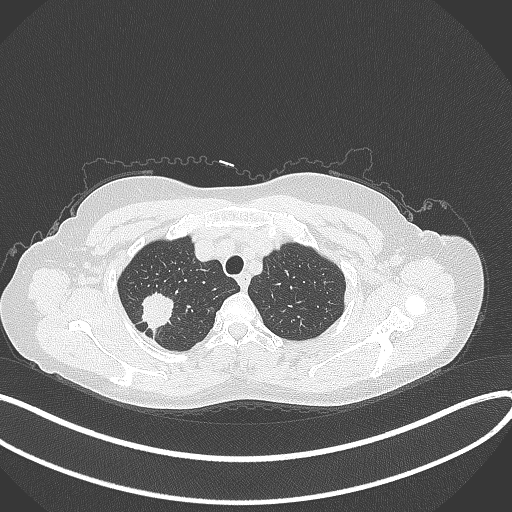
Chest CT, one axial slice. Slice 309 of 337 in the series (ordered by position). Reconstruction kernel B70f. 120 kVp. Lung window (W 1500 / L -600 HU). 512 × 512 image matrix. Patient: female, 50 years. Case-level facts recorded for this patient, not image findings: clinical TNM (as recorded): T1c N0 M0.
Outlined on this slice (bounding box drawn by a radiologist):
- lung tumour (recorded histology: adenocarcinoma): box from (x=135, y=286) to (x=177, y=334) px